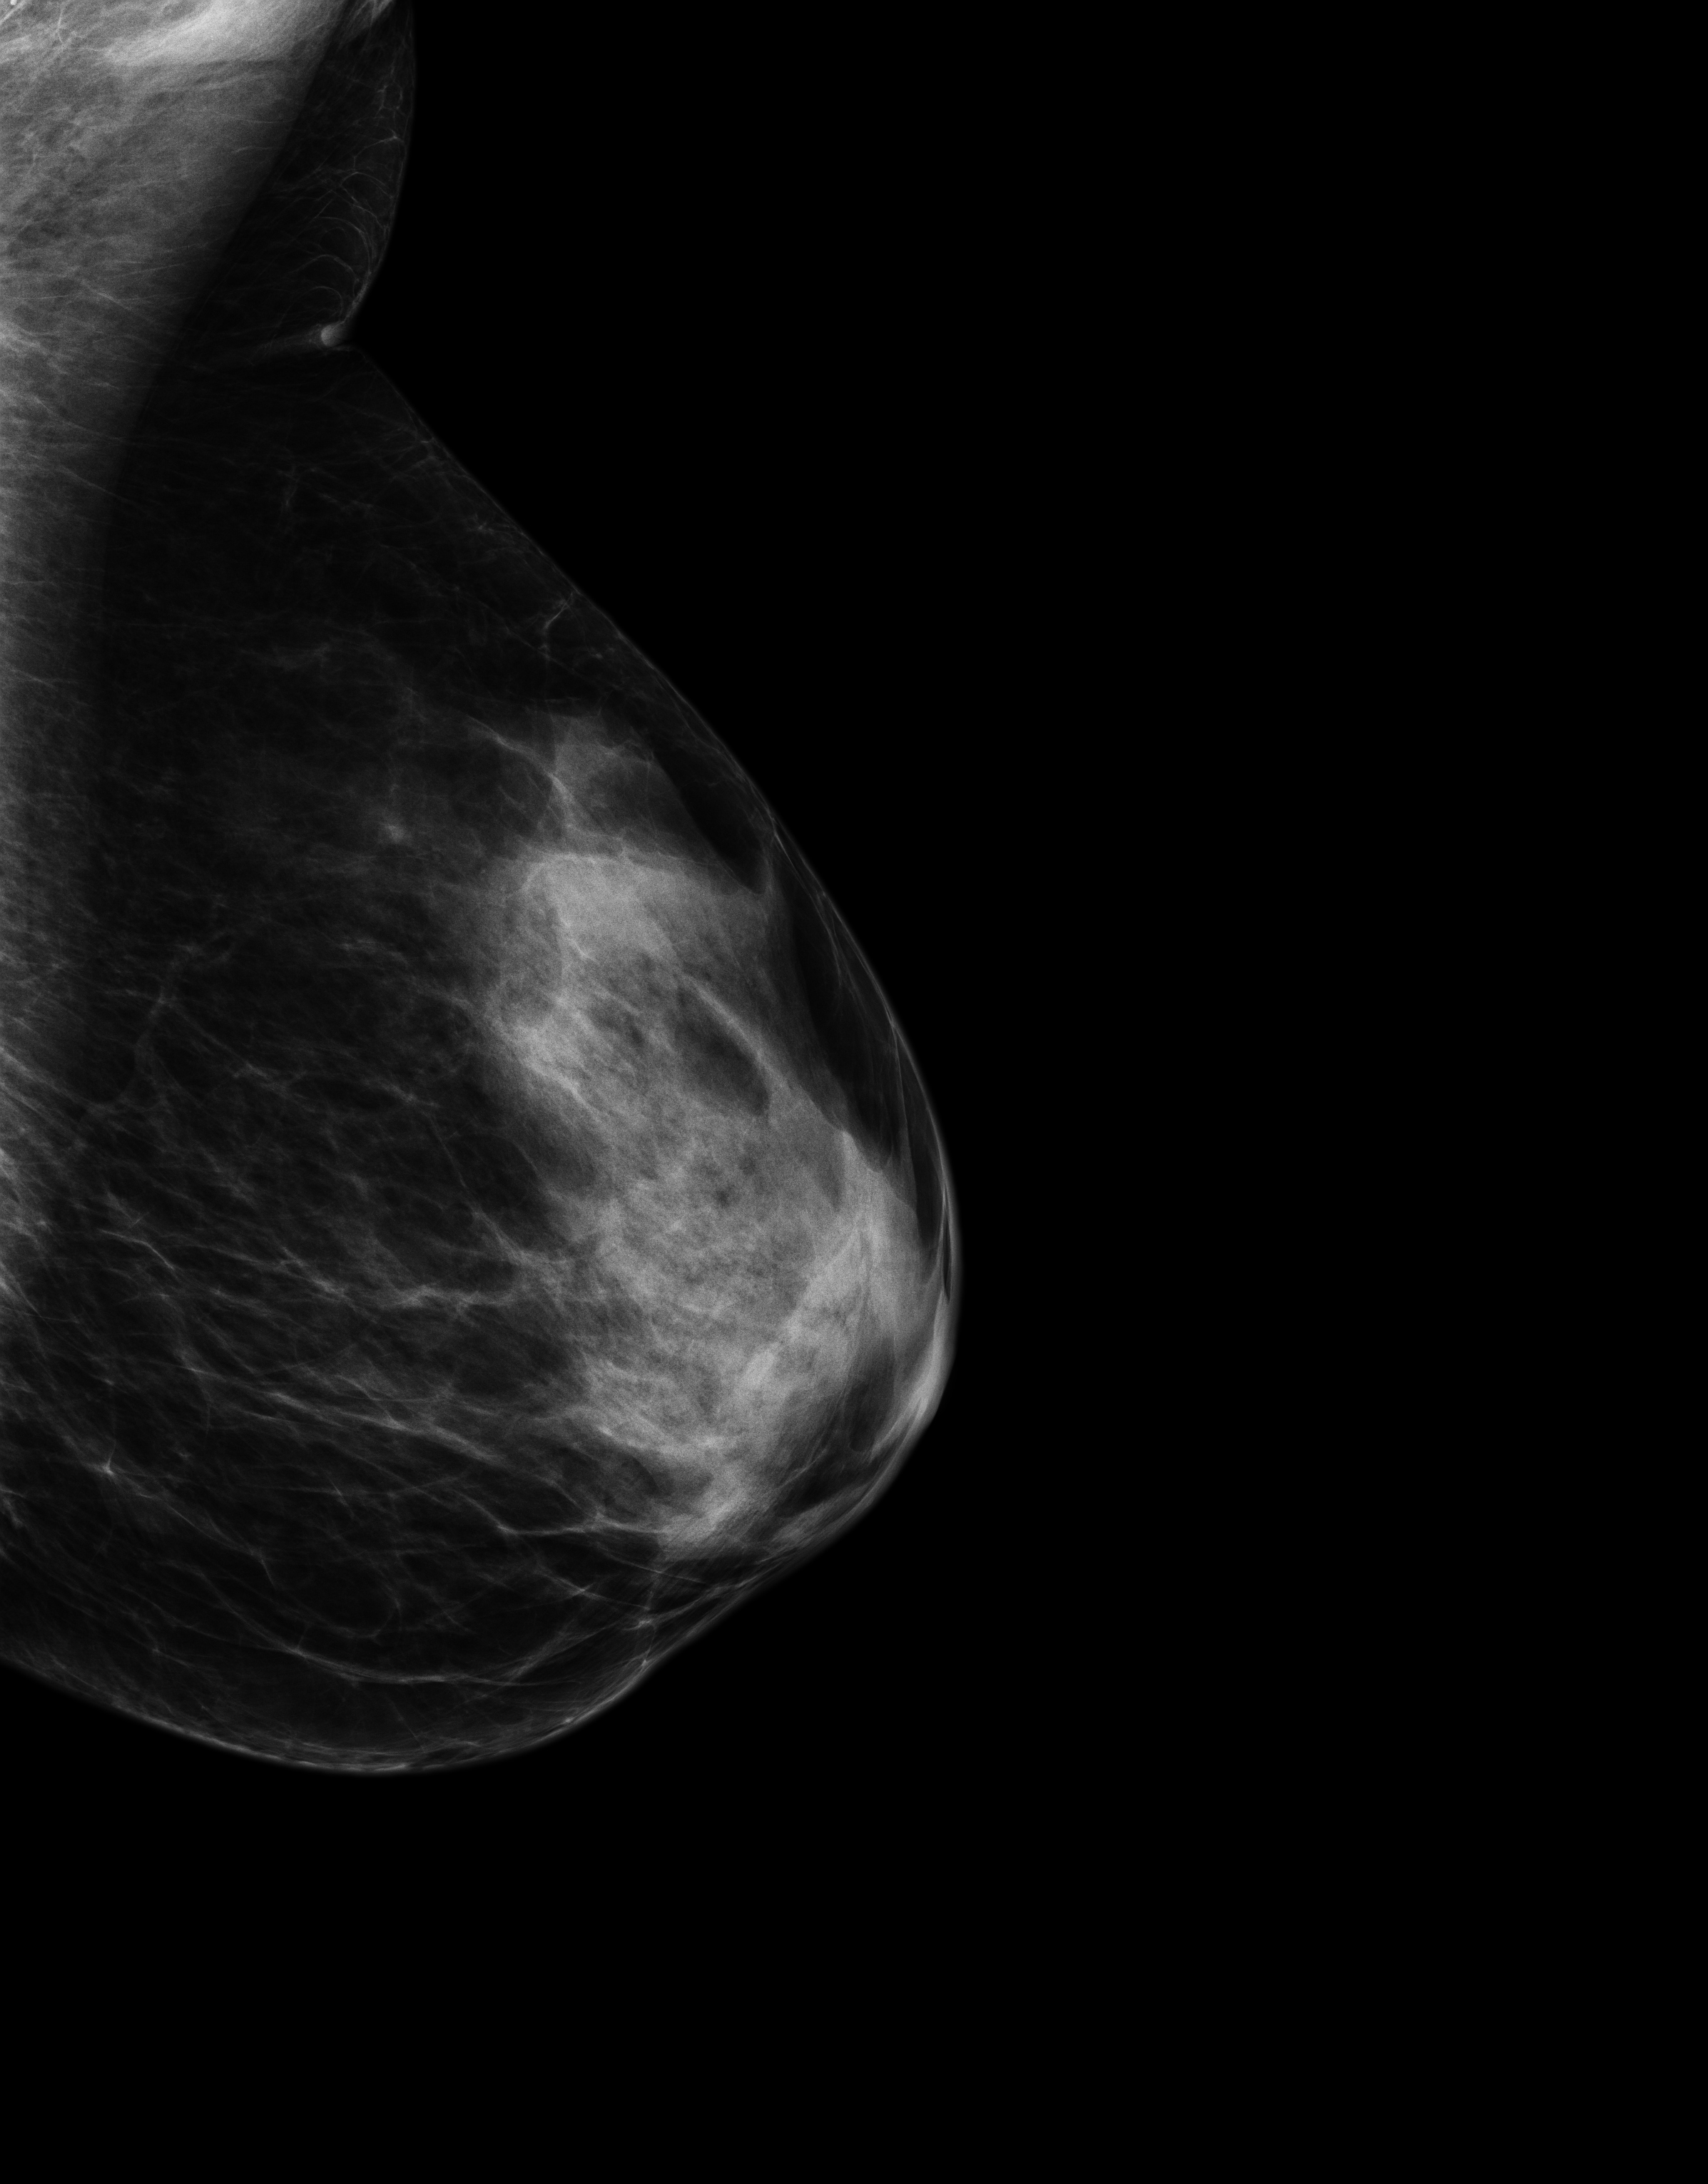
Screening examination, compressed breast thickness 43 mm. Patient: female, 49 years.
Image type: full-field digital mammogram. Breast: left. Projection: MLO view.